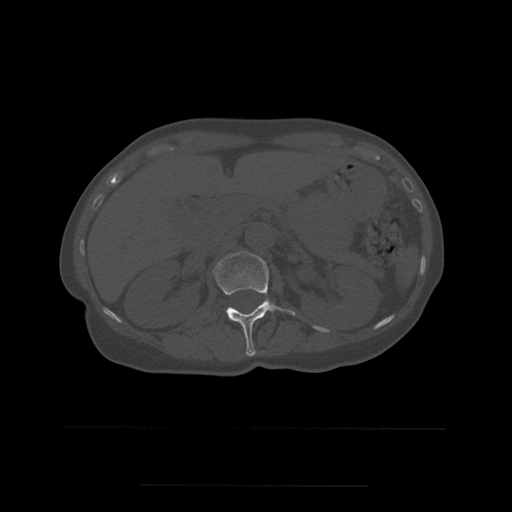
CT including the spine, one axial slice. Slice 232 of 544 in the series (ordered by position). Bone window (W 1800 / L 400 HU). 1.25 mm slice thickness. 512 × 512 image matrix, field of view 350 × 350 mm. Patient age 58 years. Case-level facts recorded for this patient, not image findings: primary cancer: lung.
Annotated regions visible in this slice (semi-automatic segmentation, software-assisted and operator-edited):
- L1 vertebra: bounding box (x1, y1, x2, y2) in pixels: (215, 252, 296, 357)